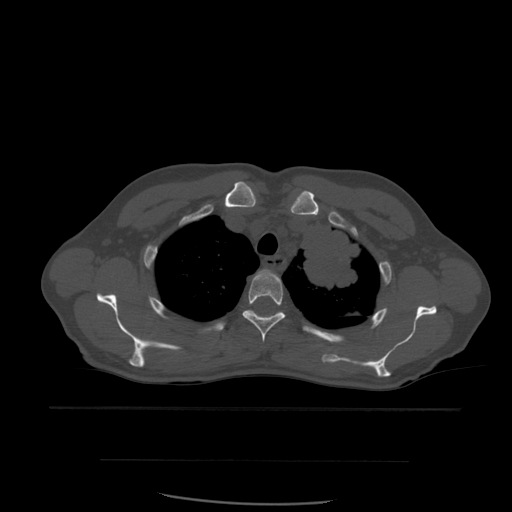
CT including the spine, one axial slice; slice 441 of 574 in the series (ordered by position); bone window (W 1800 / L 400 HU); 1.25 mm slice thickness; 512 × 512 image matrix, field of view 392 × 392 mm. Patient age 48 years. Case-level facts recorded for this patient, not image findings: primary cancer: lung; vertebrae with lytic lesions (as recorded): T11.
Annotated regions visible in this slice (semi-automatically segmented with operator editing):
- T3 vertebra: box from (x=242, y=270) to (x=286, y=343) px